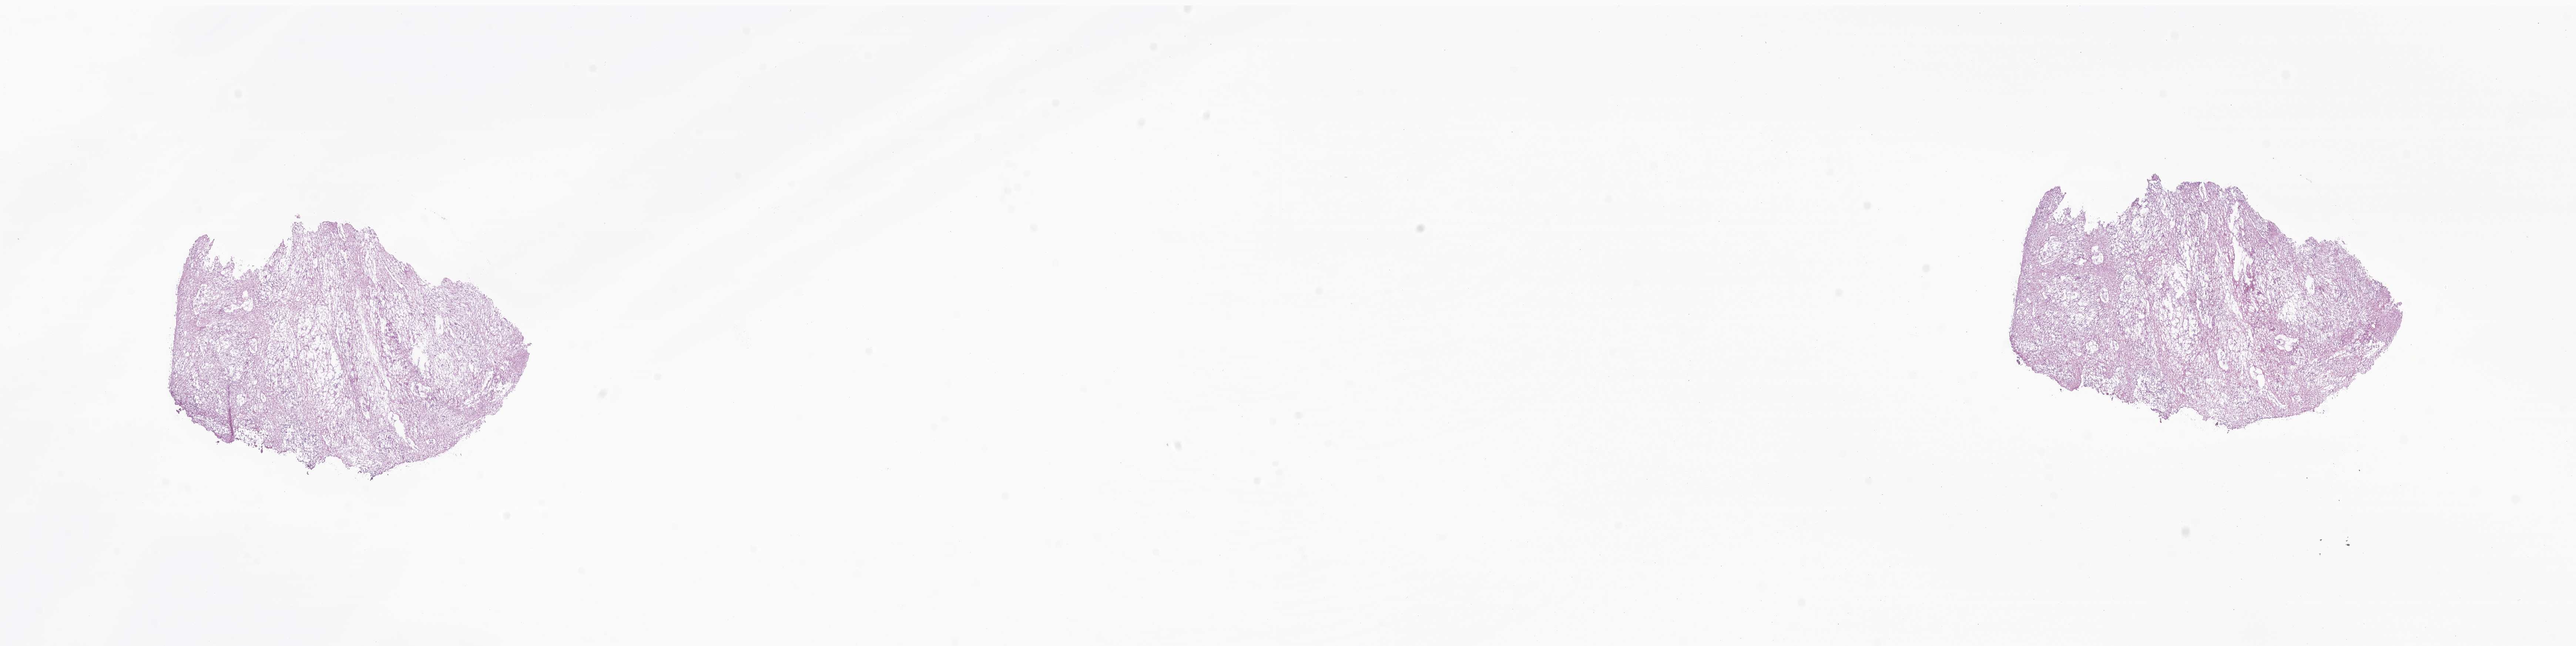
H&E whole-slide image of tumor tissue from the brain — shown as a low-resolution overview of the whole scanned area (about 29.3 x 7.4 mm); cryosection (OCT / tissue freezing medium). Patient: male, age 783 days (about 2.1 years).
• recorded diagnosis: Ependymoma, NOS